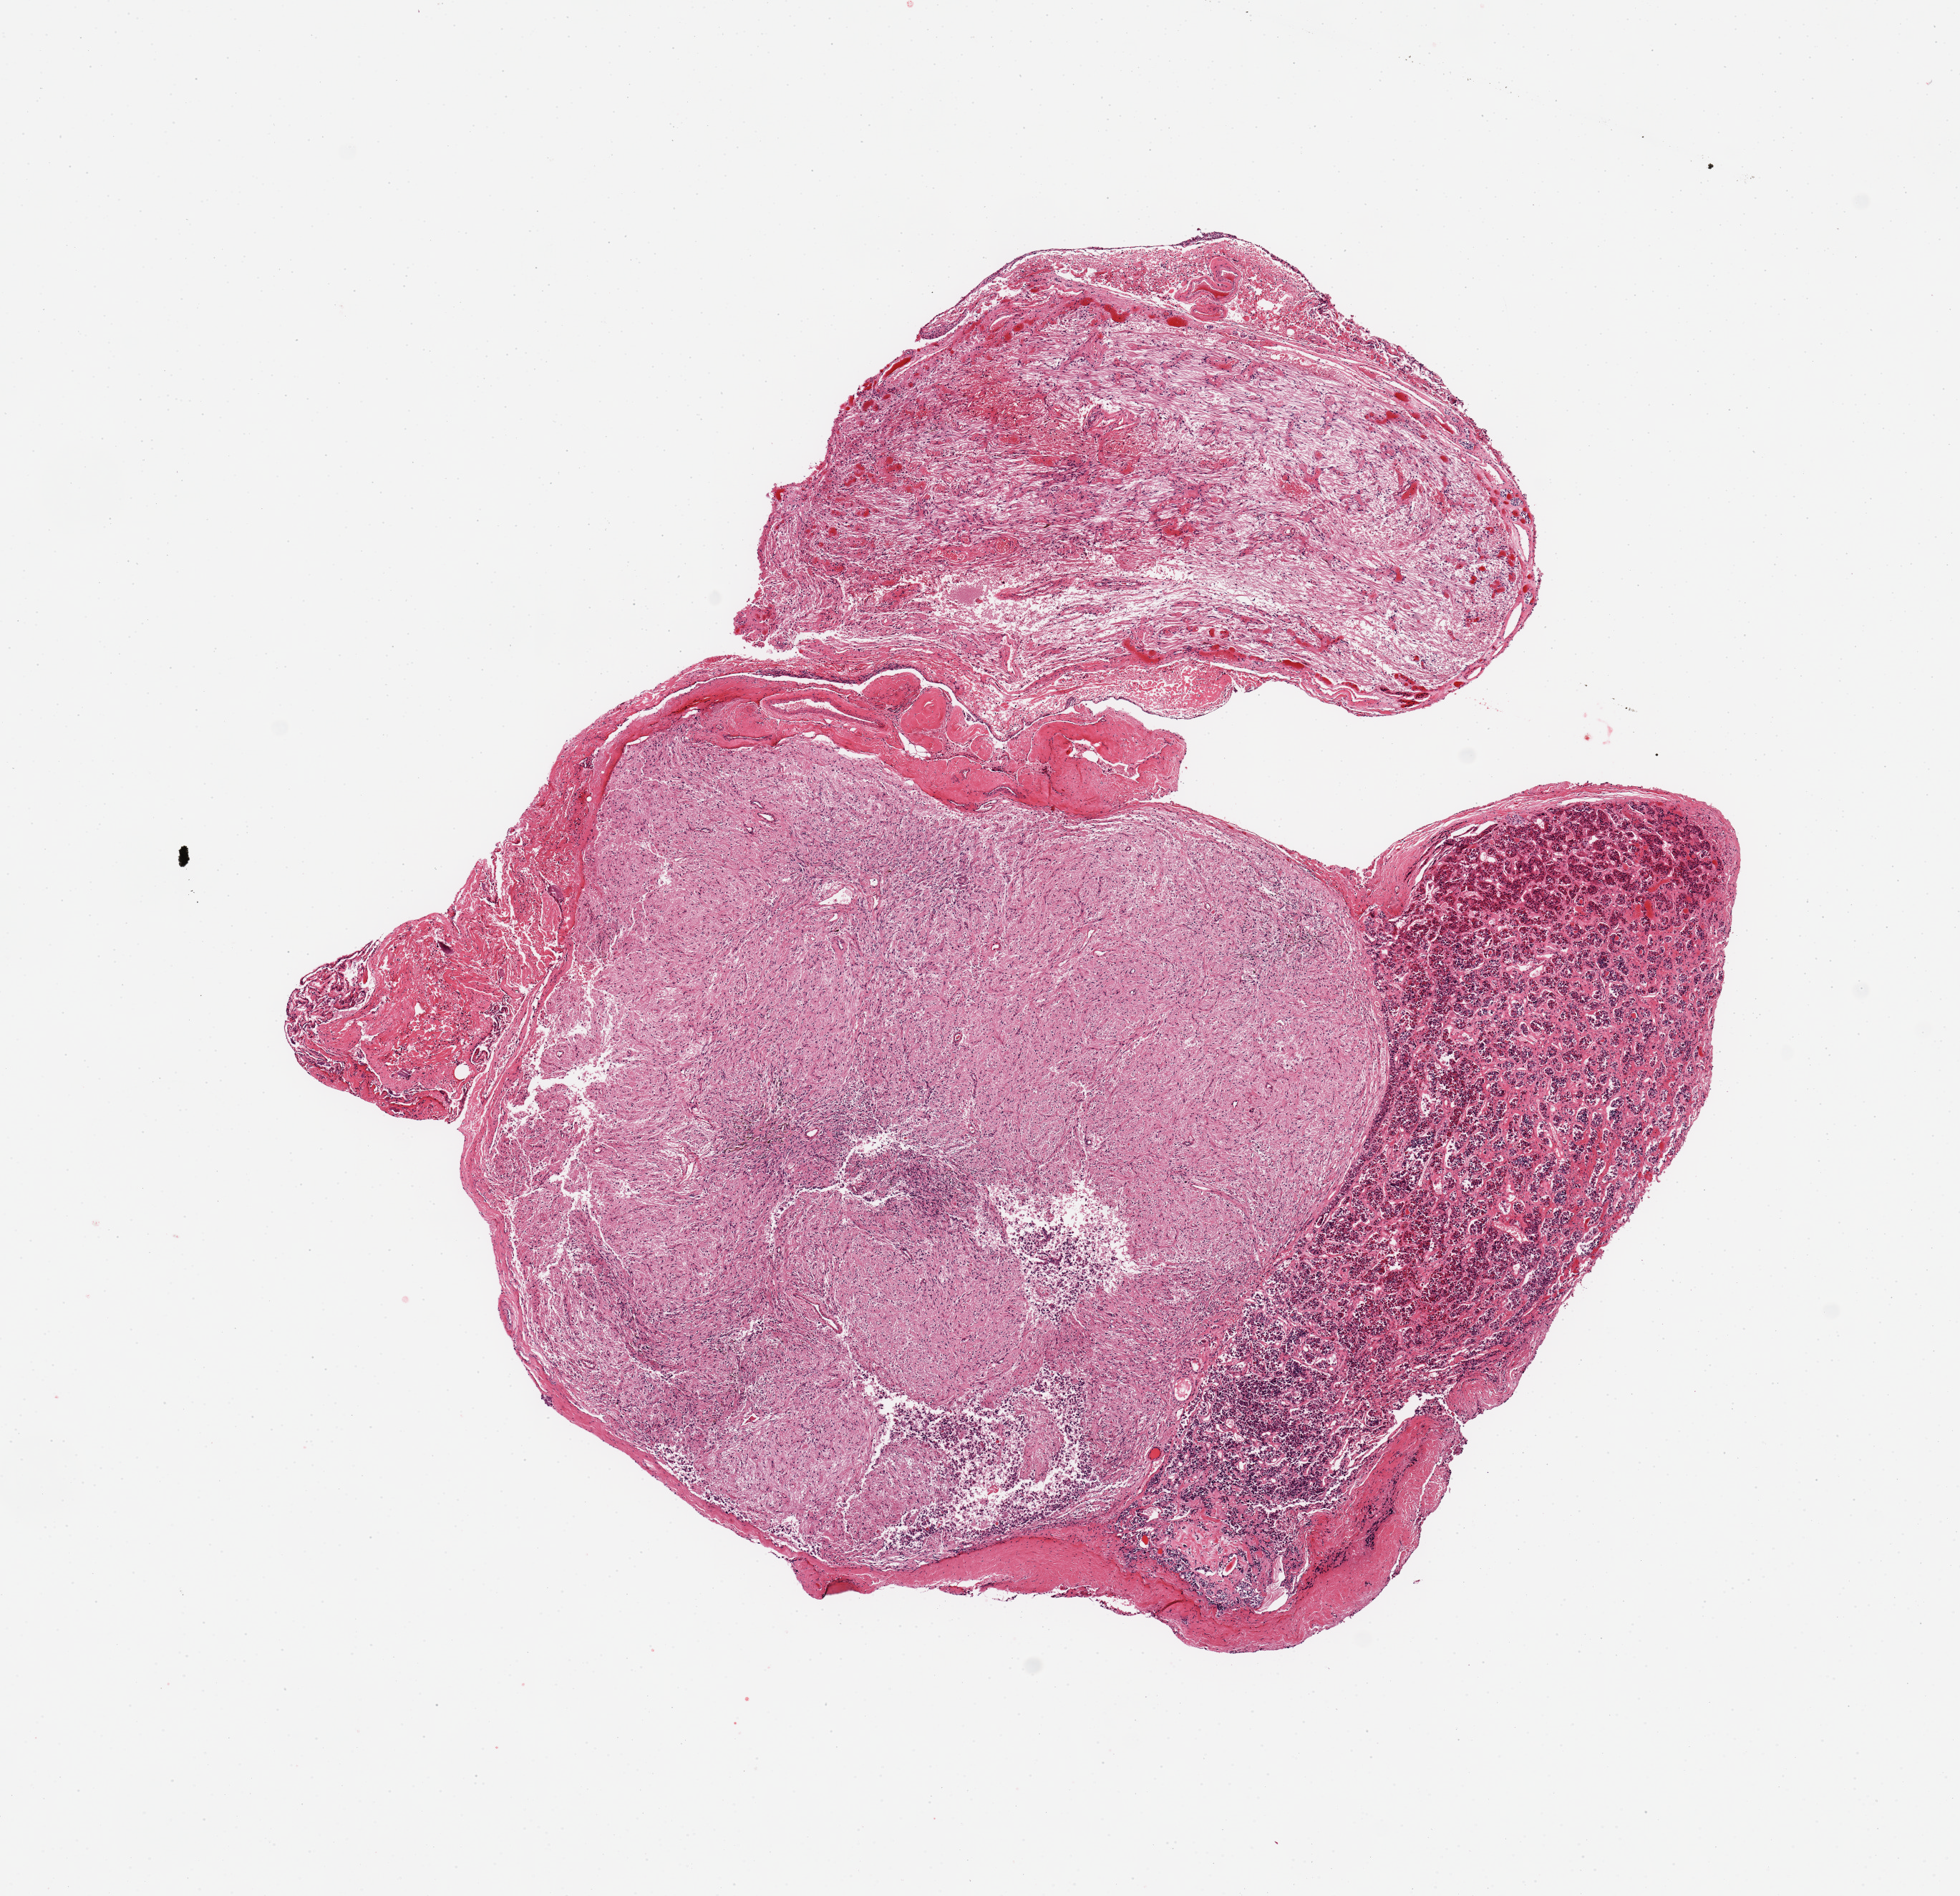
Digitized hematoxylin and eosin (H&E)-stained section, shown as a low-resolution overview of the whole scanned area (about 10.8 x 10.5 mm). Donor sex: male.
* specimen: PAXgene-fixed, paraffin-embedded tissue; section of pituitary (target tissue); tissue donor sample